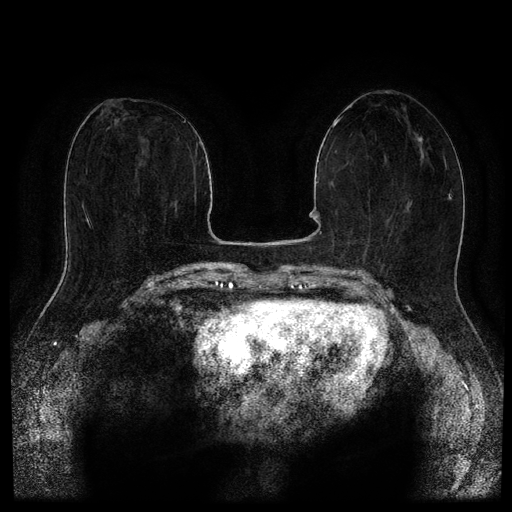
Breast MRI (dynamic contrast-enhanced, multi-phase), one axial slice; slice 51 of 116 in the series (ordered by position); dynamic contrast-enhanced series, time point 2 of 5 at this slice position (early post-contrast); 1.5 T; TE 2.6 ms, TR 5.3 ms; 512 × 512 image matrix, field of view 350 × 350 mm. Patient: female, 66 years.
Structures marked on this image (semi-automatically segmented with operator editing):
- breast lesion (labelled benign in the annotation): bounding box (x1, y1, x2, y2) in pixels: (405, 202, 411, 212)